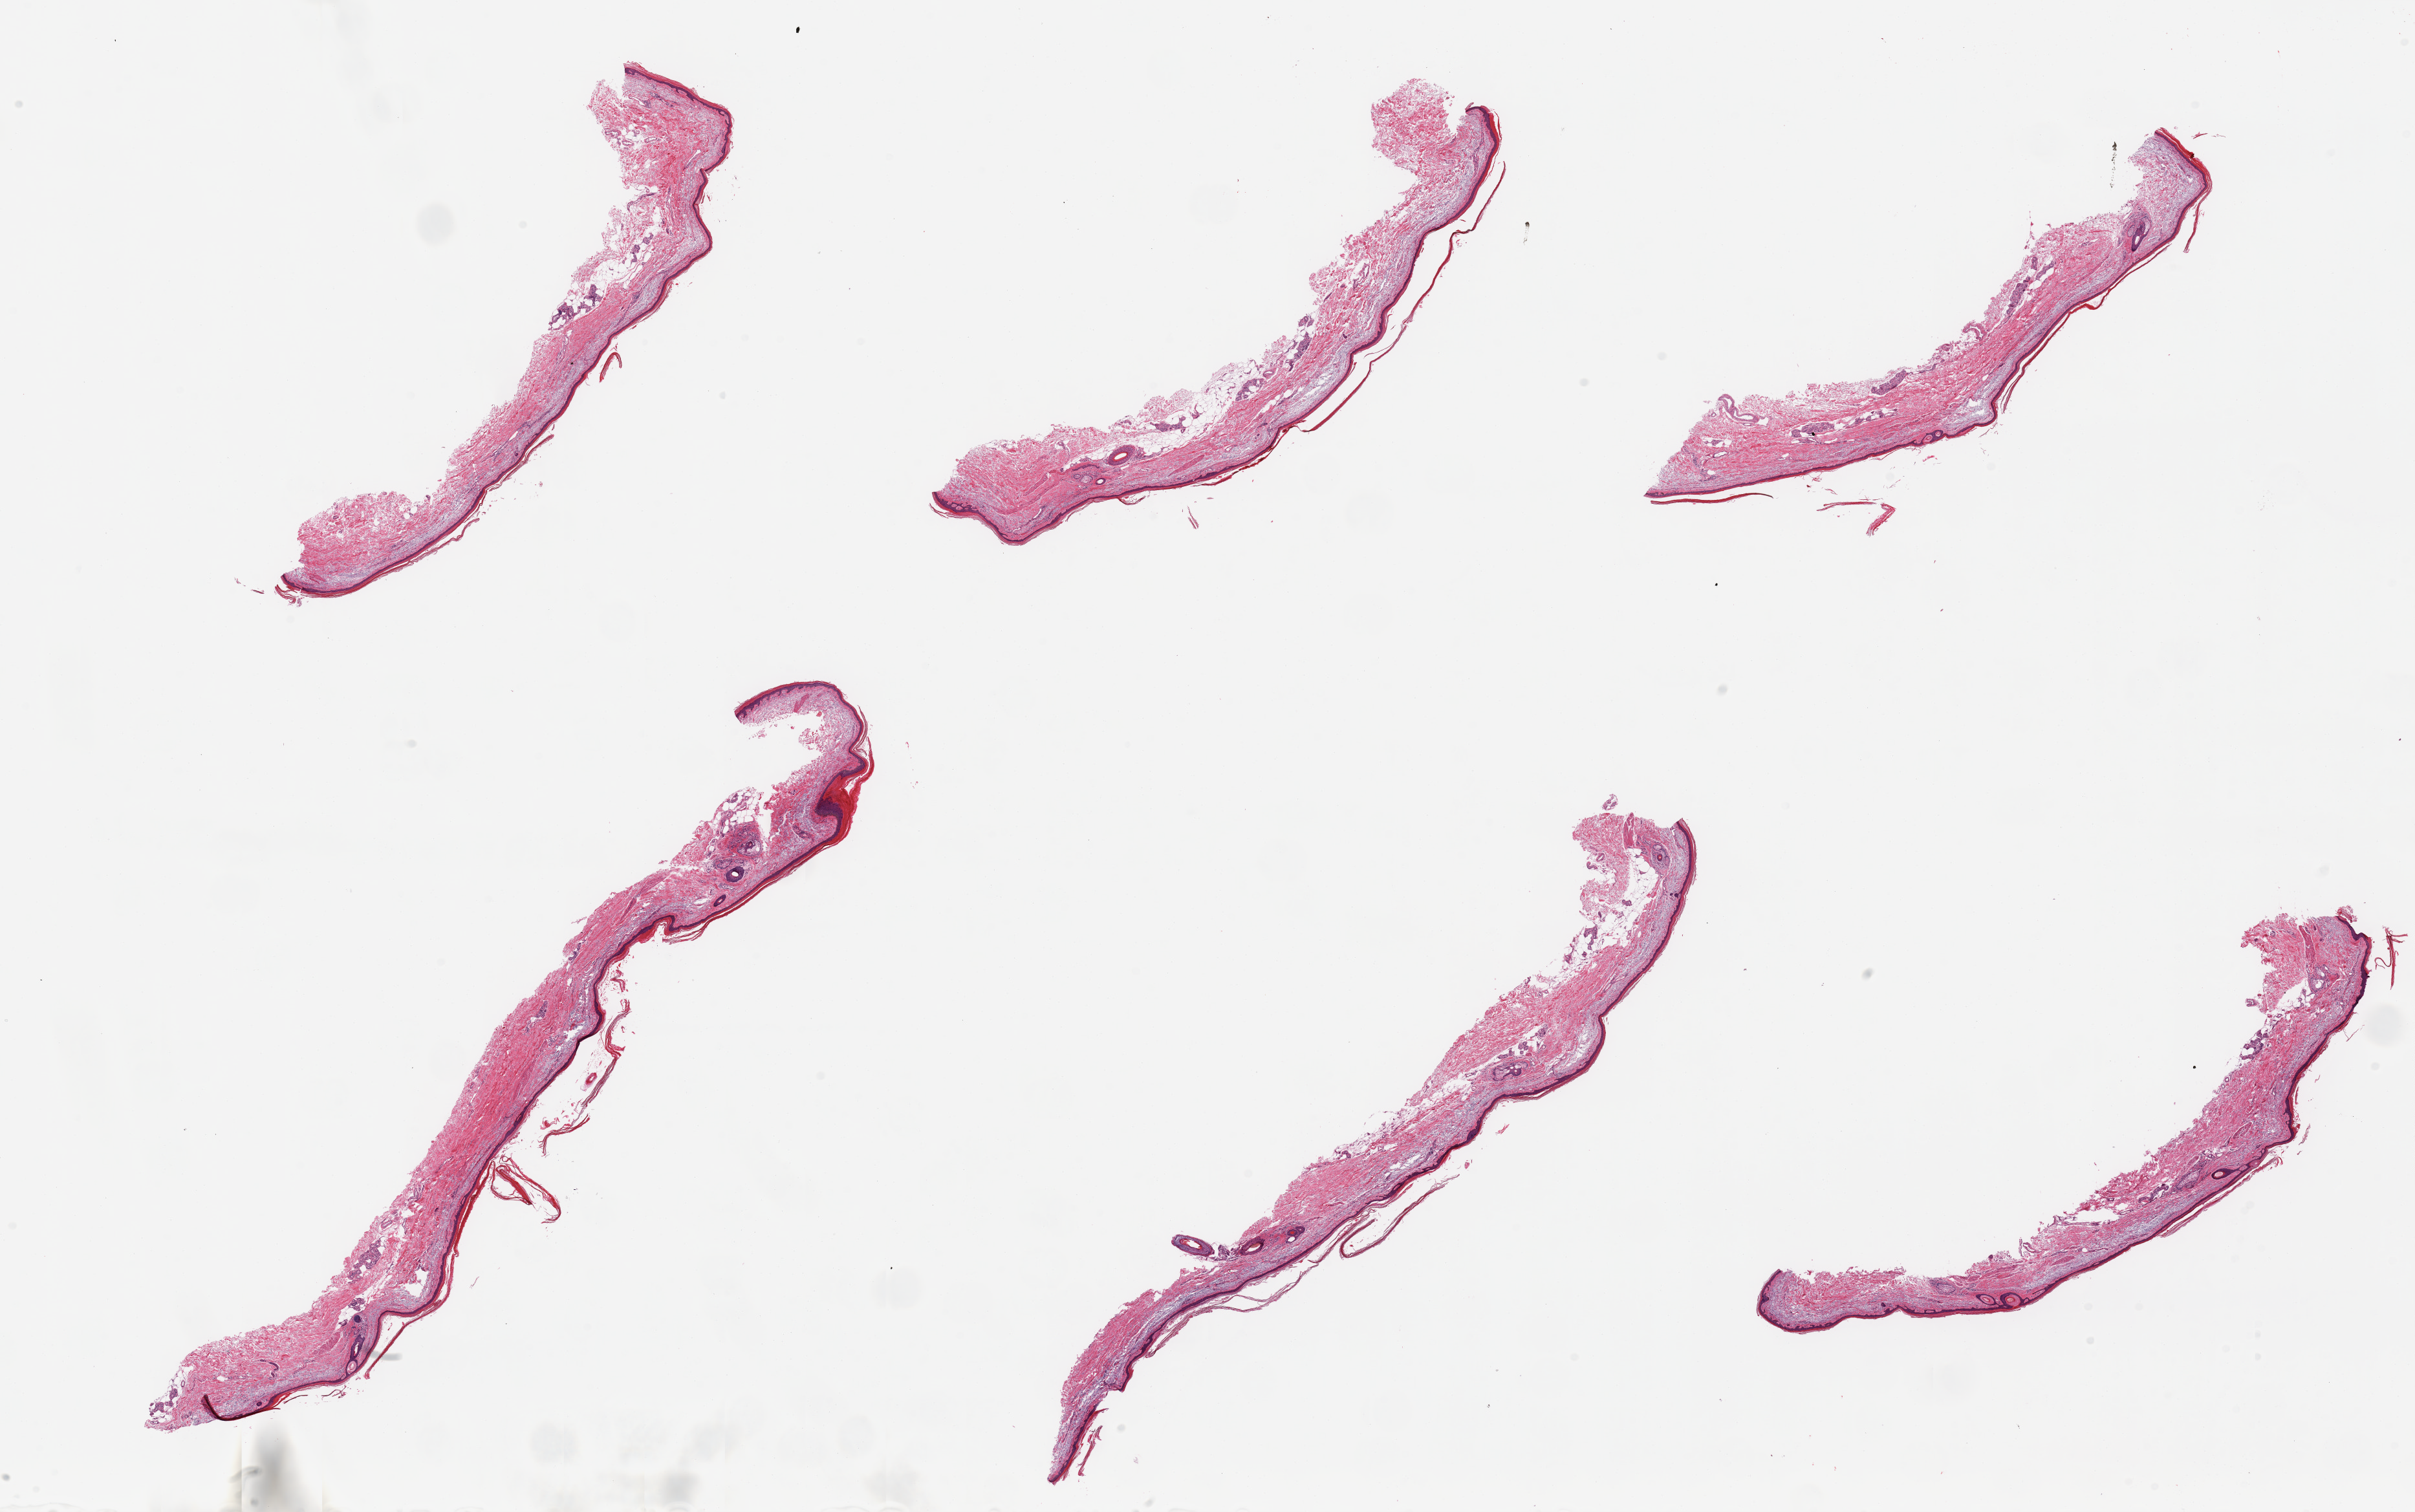
Digitized hematoxylin and eosin (H&E)-stained section, brightfield — whole scanned area (about 29.5 x 18.5 mm, acquisition: 20x scan) shown as a low-resolution overview. PAXgene-fixed, paraffin-embedded tissue. Target tissue: skin of lower leg. Tissue donor sample.
Reviewer comment on this tissue sample: 6 pieces; no dermal fat; squamous epithelium is ~30 microns. Notable dermal solar elastosis.